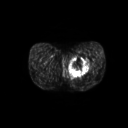
FDG PET of an extremity soft-tissue mass (from a PET/CT study), one axial slice. Position 29 of 267 along the scan axis. 3.27 mm slice thickness. 128 × 128 image matrix, field of view 600 × 600 mm. Male patient, age 59 years. Case-level facts recorded for this patient, not image findings: histological type: pleiomorphic liposarcoma; grade: high; site of the primary tumour: left thigh.
Annotated regions visible in this slice (expert contour drawn on MRI and transferred to this co-registered scan by the dataset authors):
- gross tumour volume including surrounding oedema: bounding box [x1, y1, x2, y2] px = [69, 56, 91, 78]
- gross tumour volume (mass): [70, 57, 90, 76]